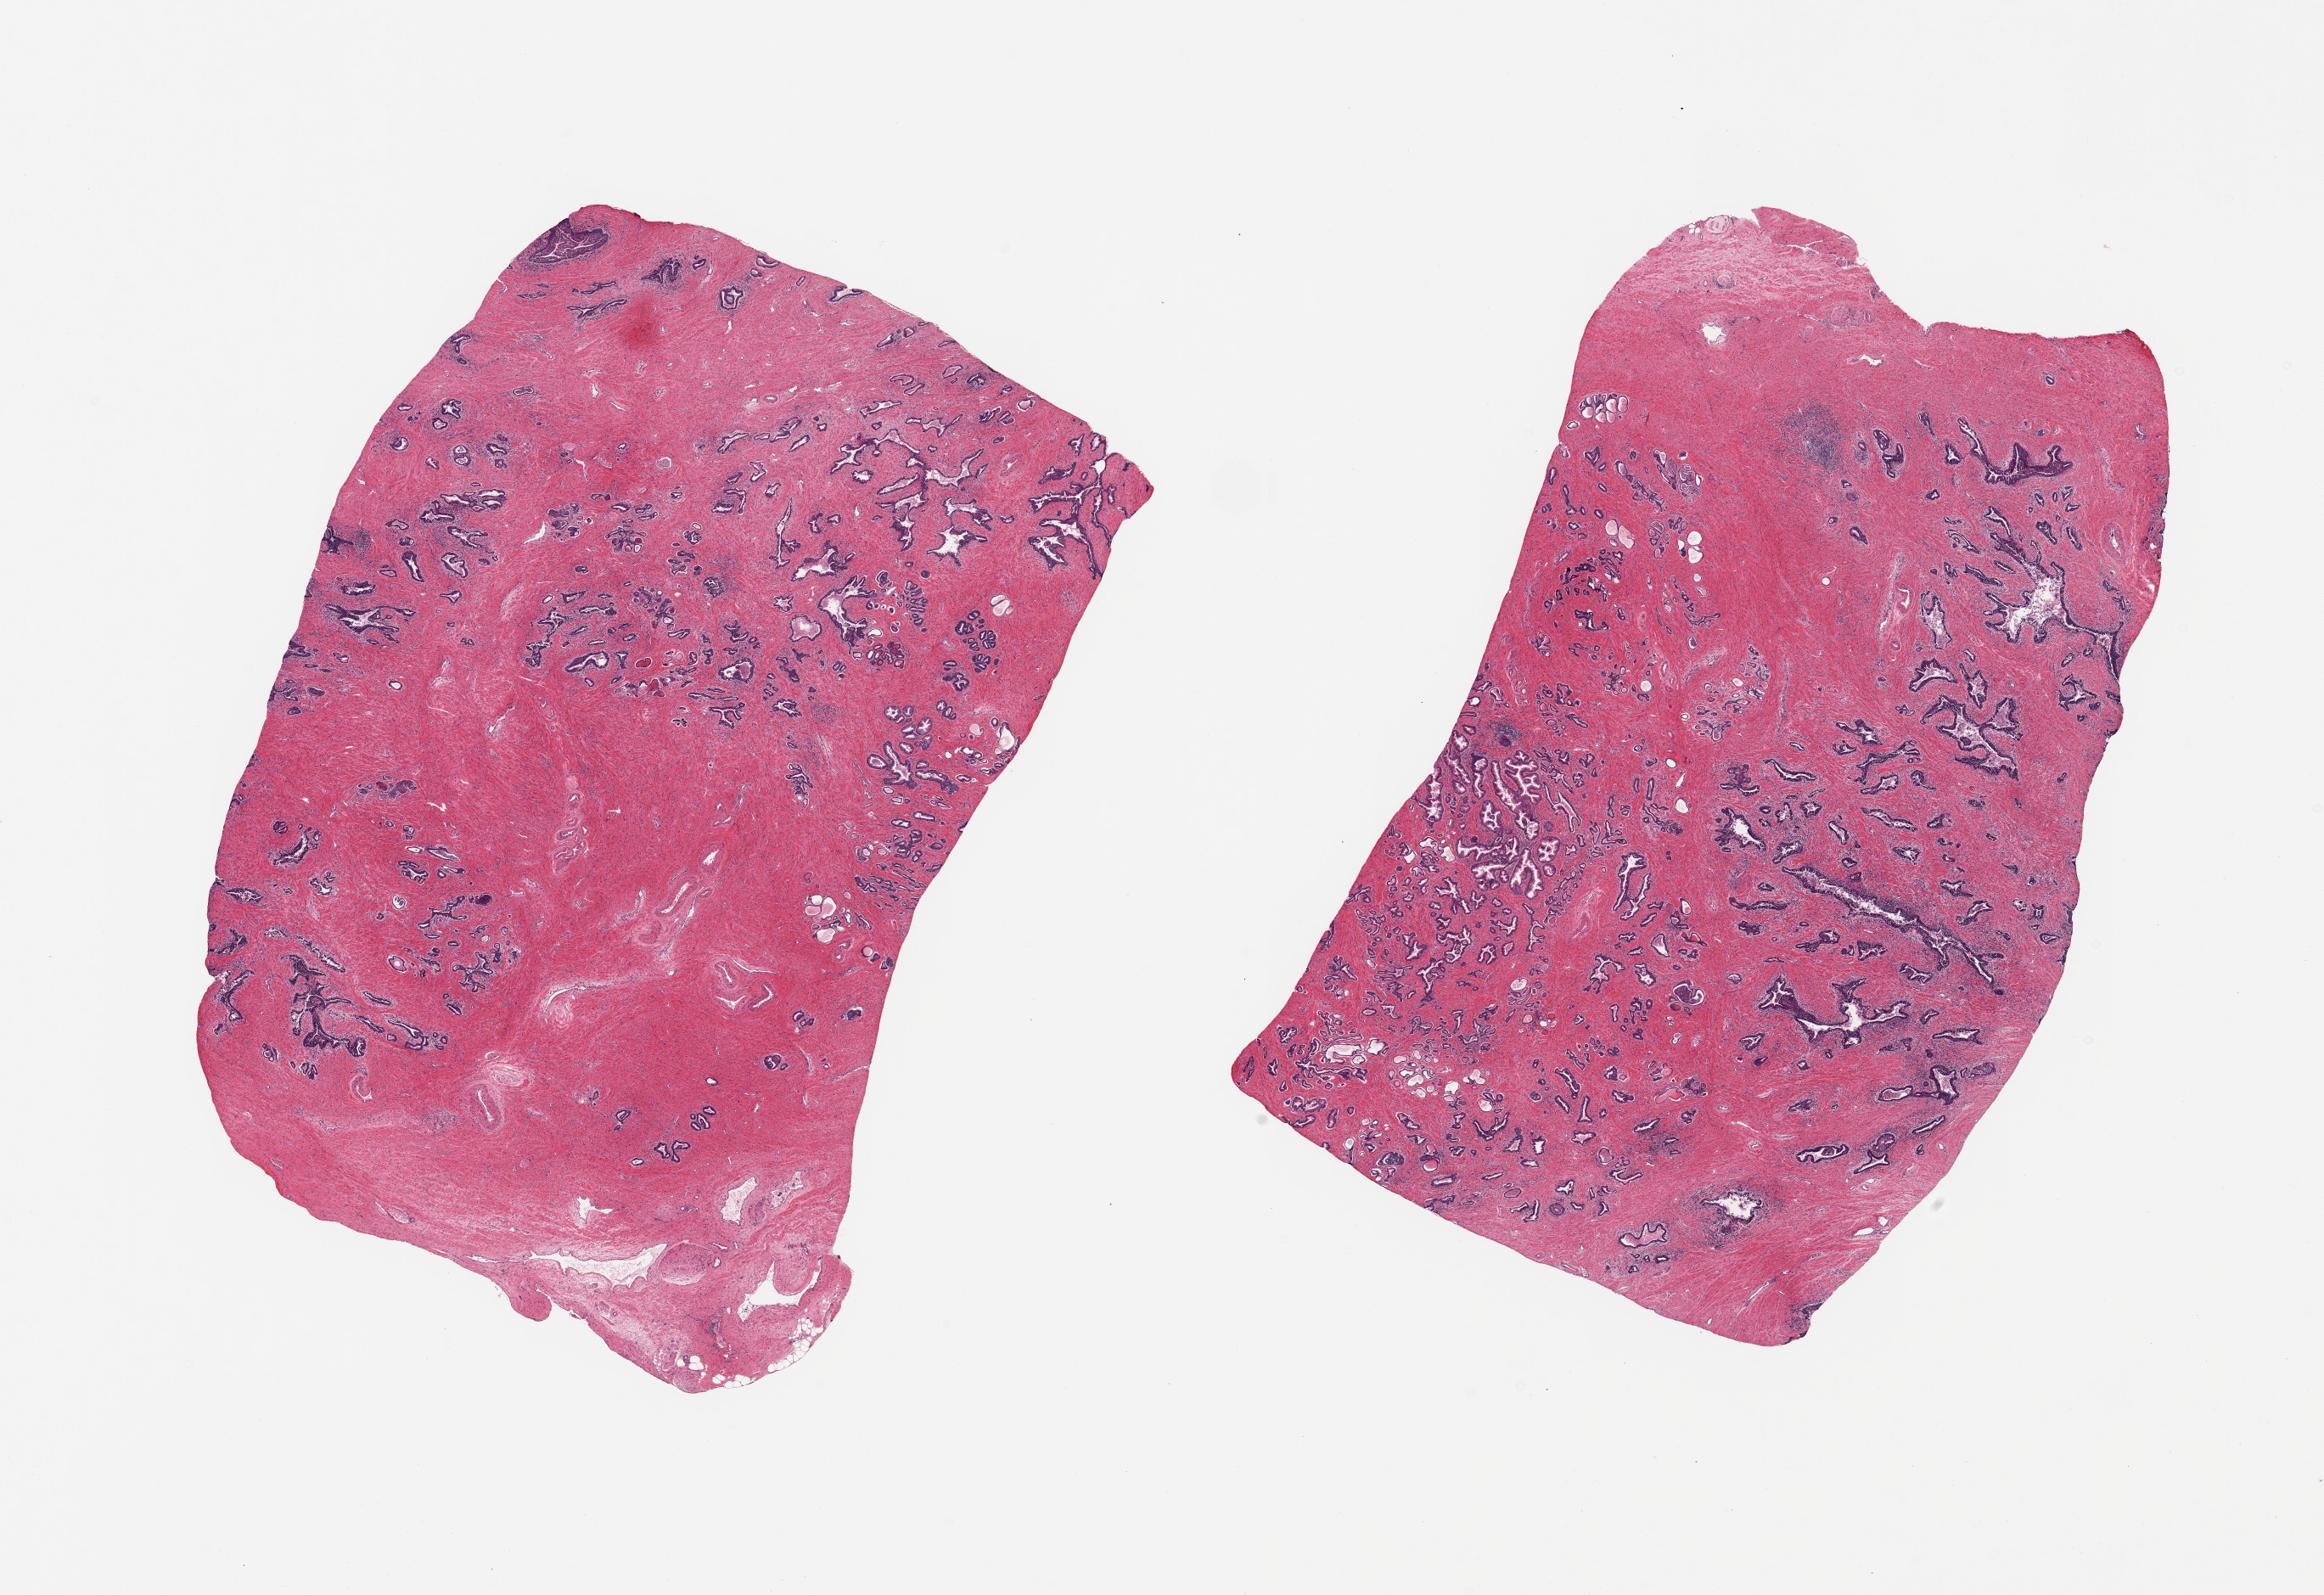
Hematoxylin and eosin (H&E) whole-slide image, shown as a low-resolution overview of the whole scanned area (about 21.7 x 14.9 mm). PAXgene-fixed paraffin-embedded (PFPE) section. Target tissue: prostate. Donor tissue sample.
• reviewer comment on this tissue sample: 2 pieces; mild acute and chronic prostatitis